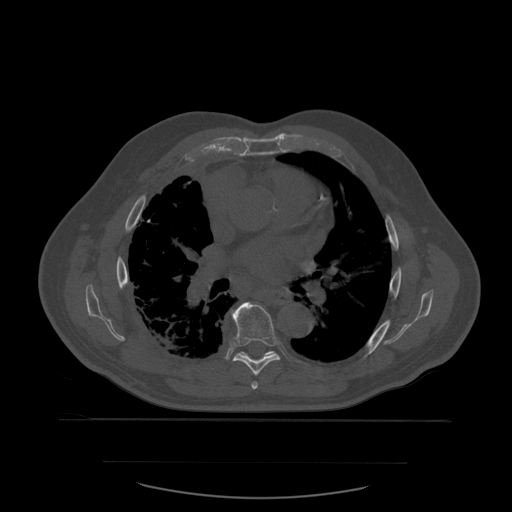
CT including the spine, one axial slice. Slice 381 of 590 in the series (ordered by position). Bone window (W 1800 / L 400 HU). 1.25 mm slice thickness. 512 × 512 image matrix, field of view 479 × 479 mm. Patient age 71 years. Case-level facts recorded for this patient, not image findings: primary cancer: lung.
Annotated regions visible in this slice (semi-automatically segmented with operator editing):
- T6 vertebra: box from (x=252, y=382) to (x=258, y=390) px
- T7 vertebra: (x=230, y=302)–(x=281, y=377)